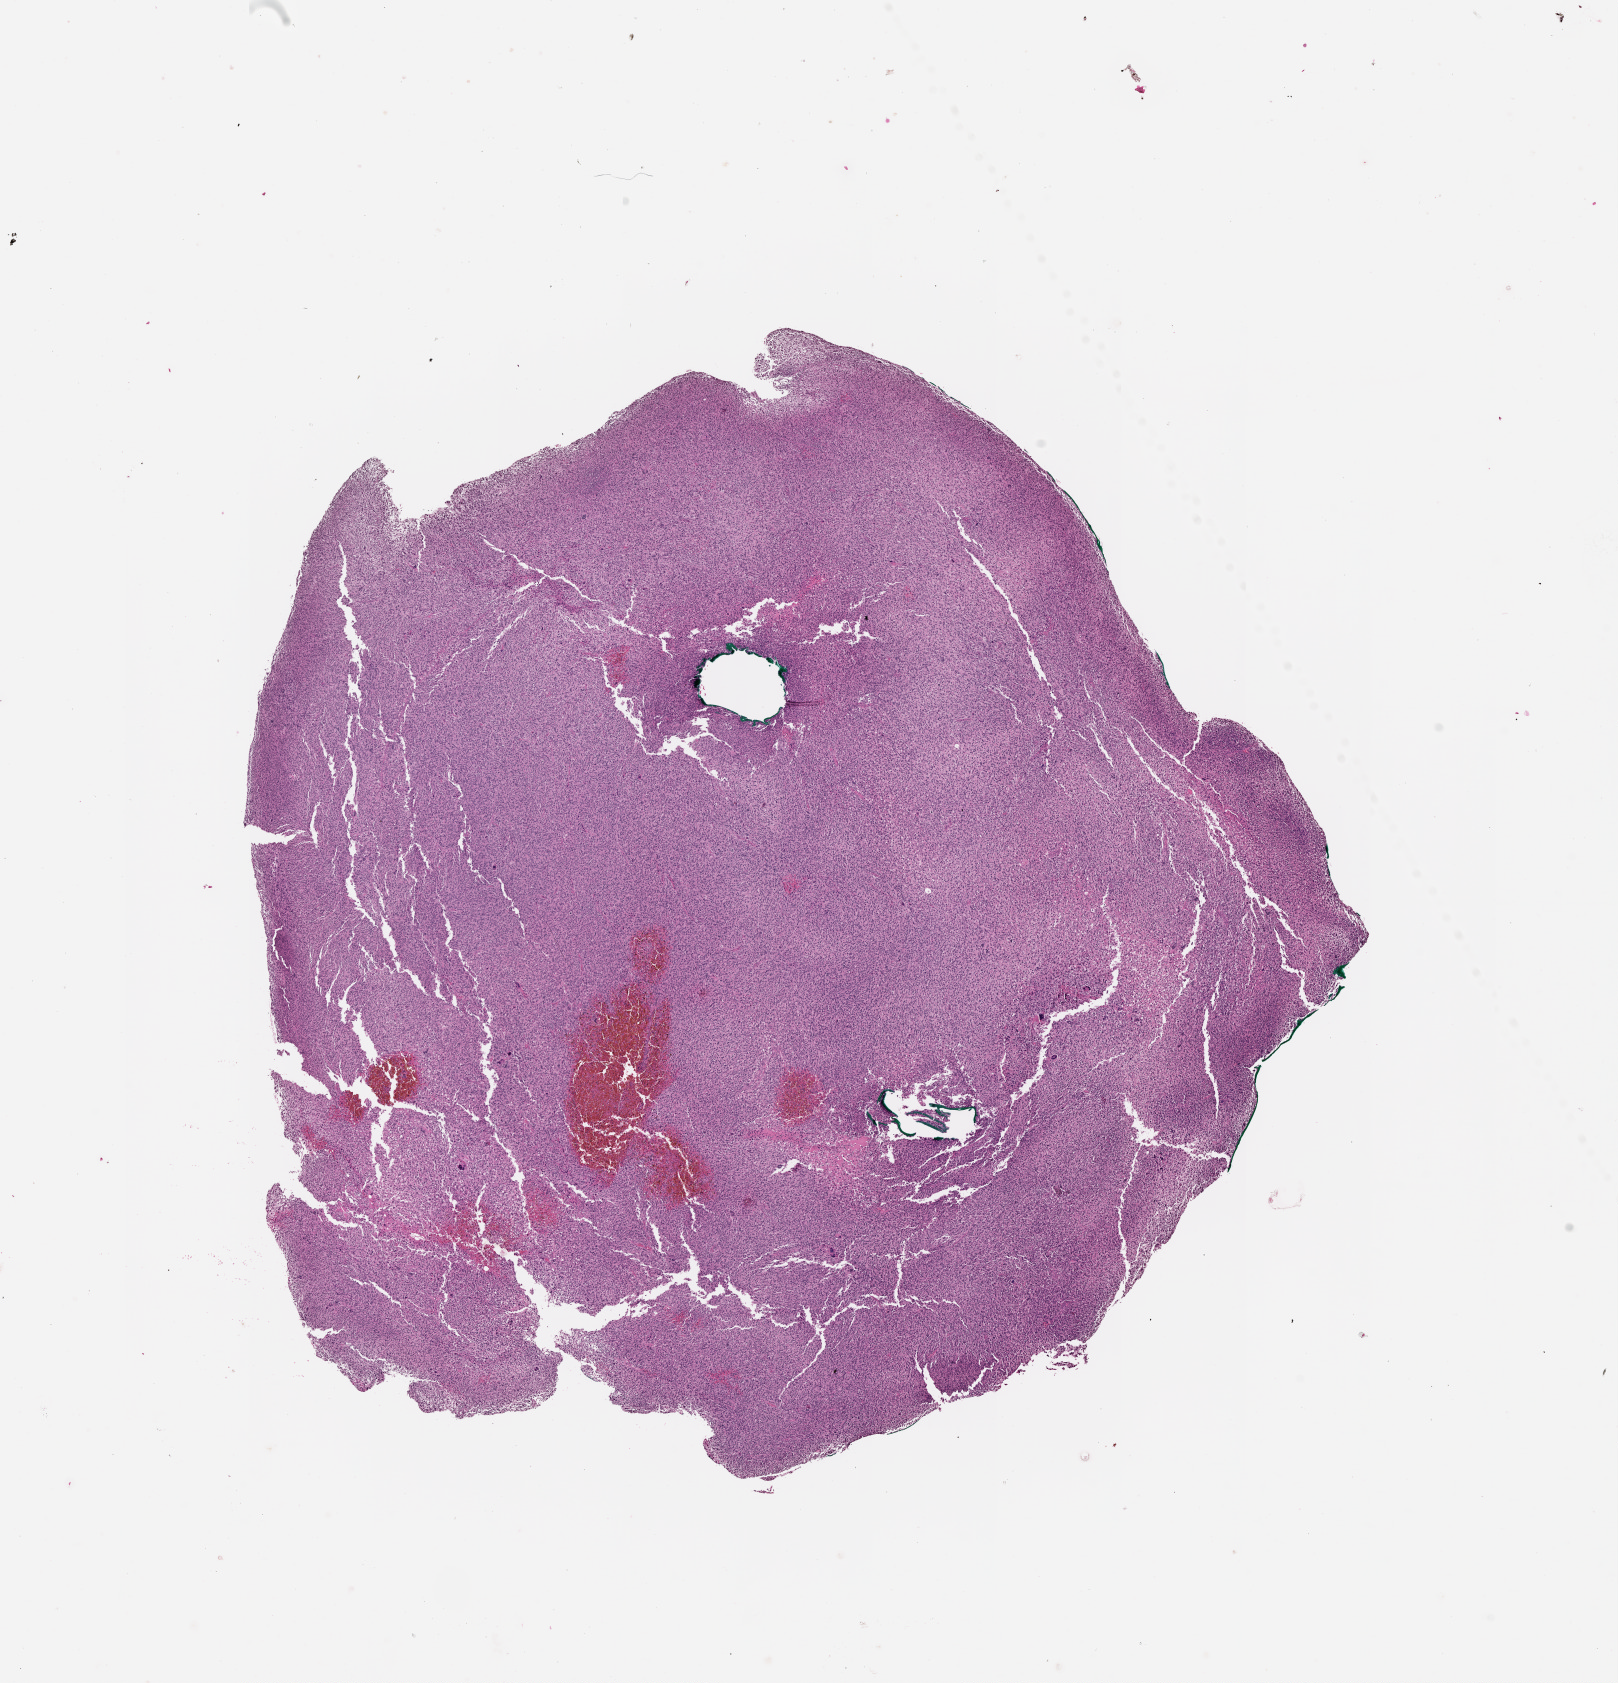
H&E-stained whole-slide image — low-resolution overview of the scanned area, about 13.0 x 13.6 mm.
• patient diagnosis (cohort enrolment): sarcoma (site not recorded at cohort level)